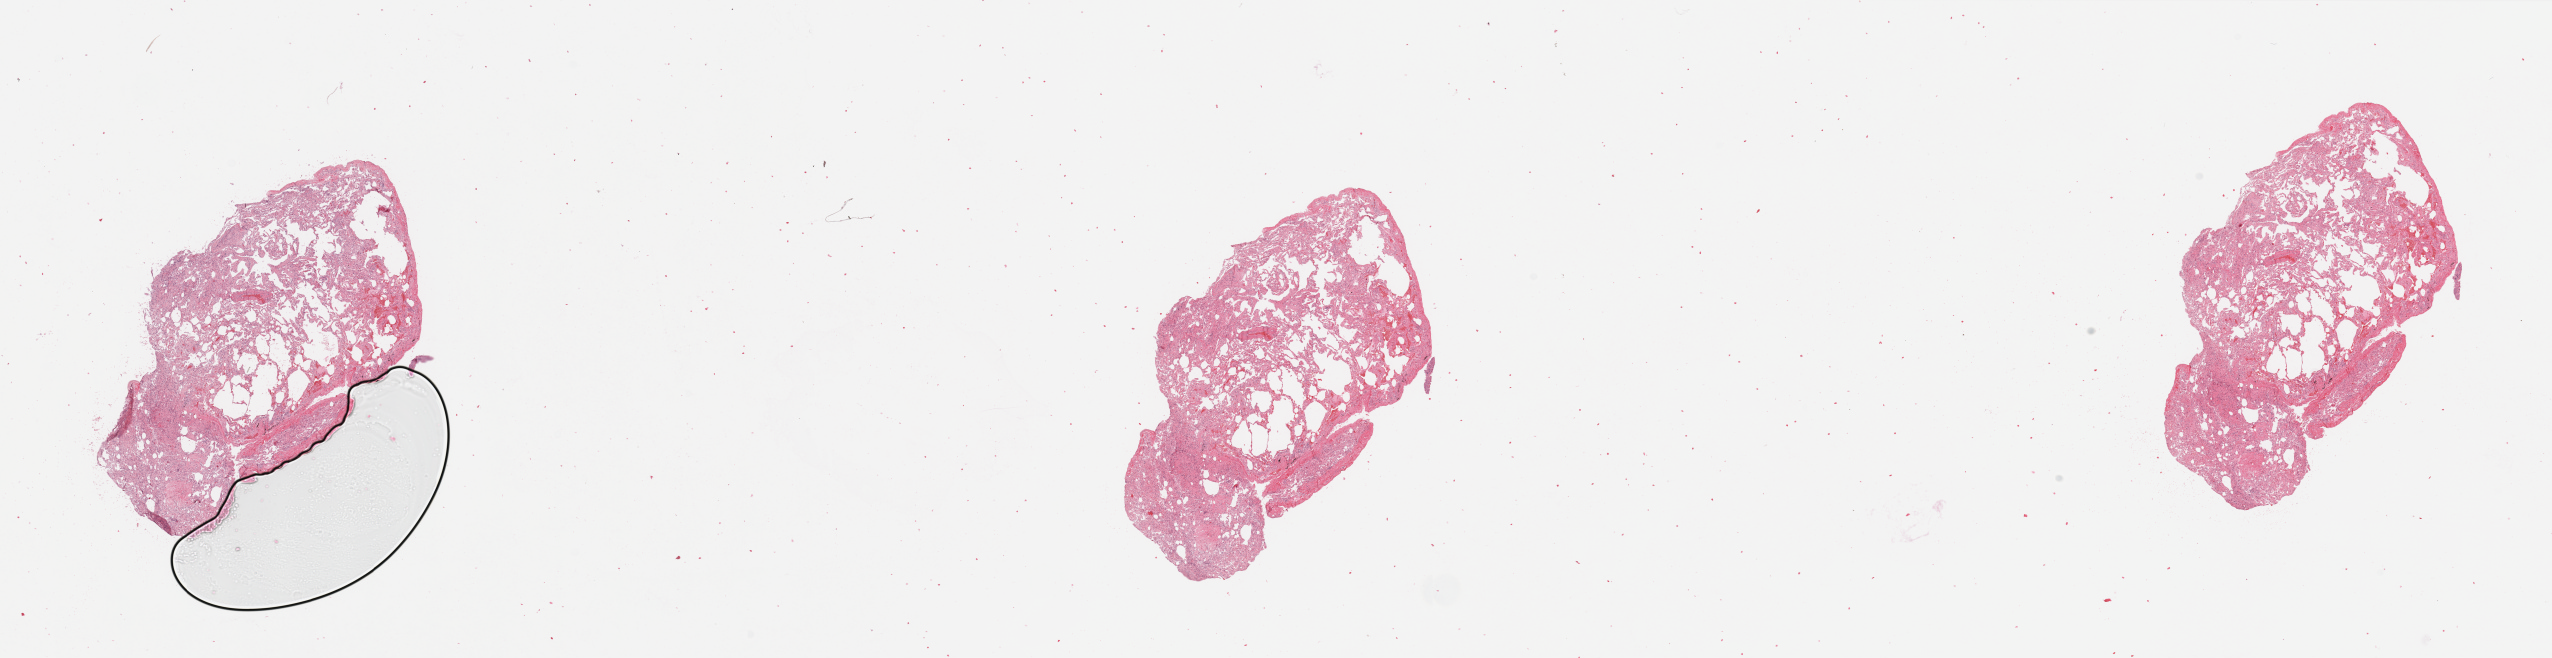
H&E-stained whole-slide image, whole scanned area (about 40.4 x 10.4 mm, from a 20x scan) shown as a low-resolution overview; lung, normal (non-tumour) tissue. 66-year-old male patient.
- this section: normal (non-tumour) tissue from the same patient
- patient diagnosis: Adenocarcinoma, NOS